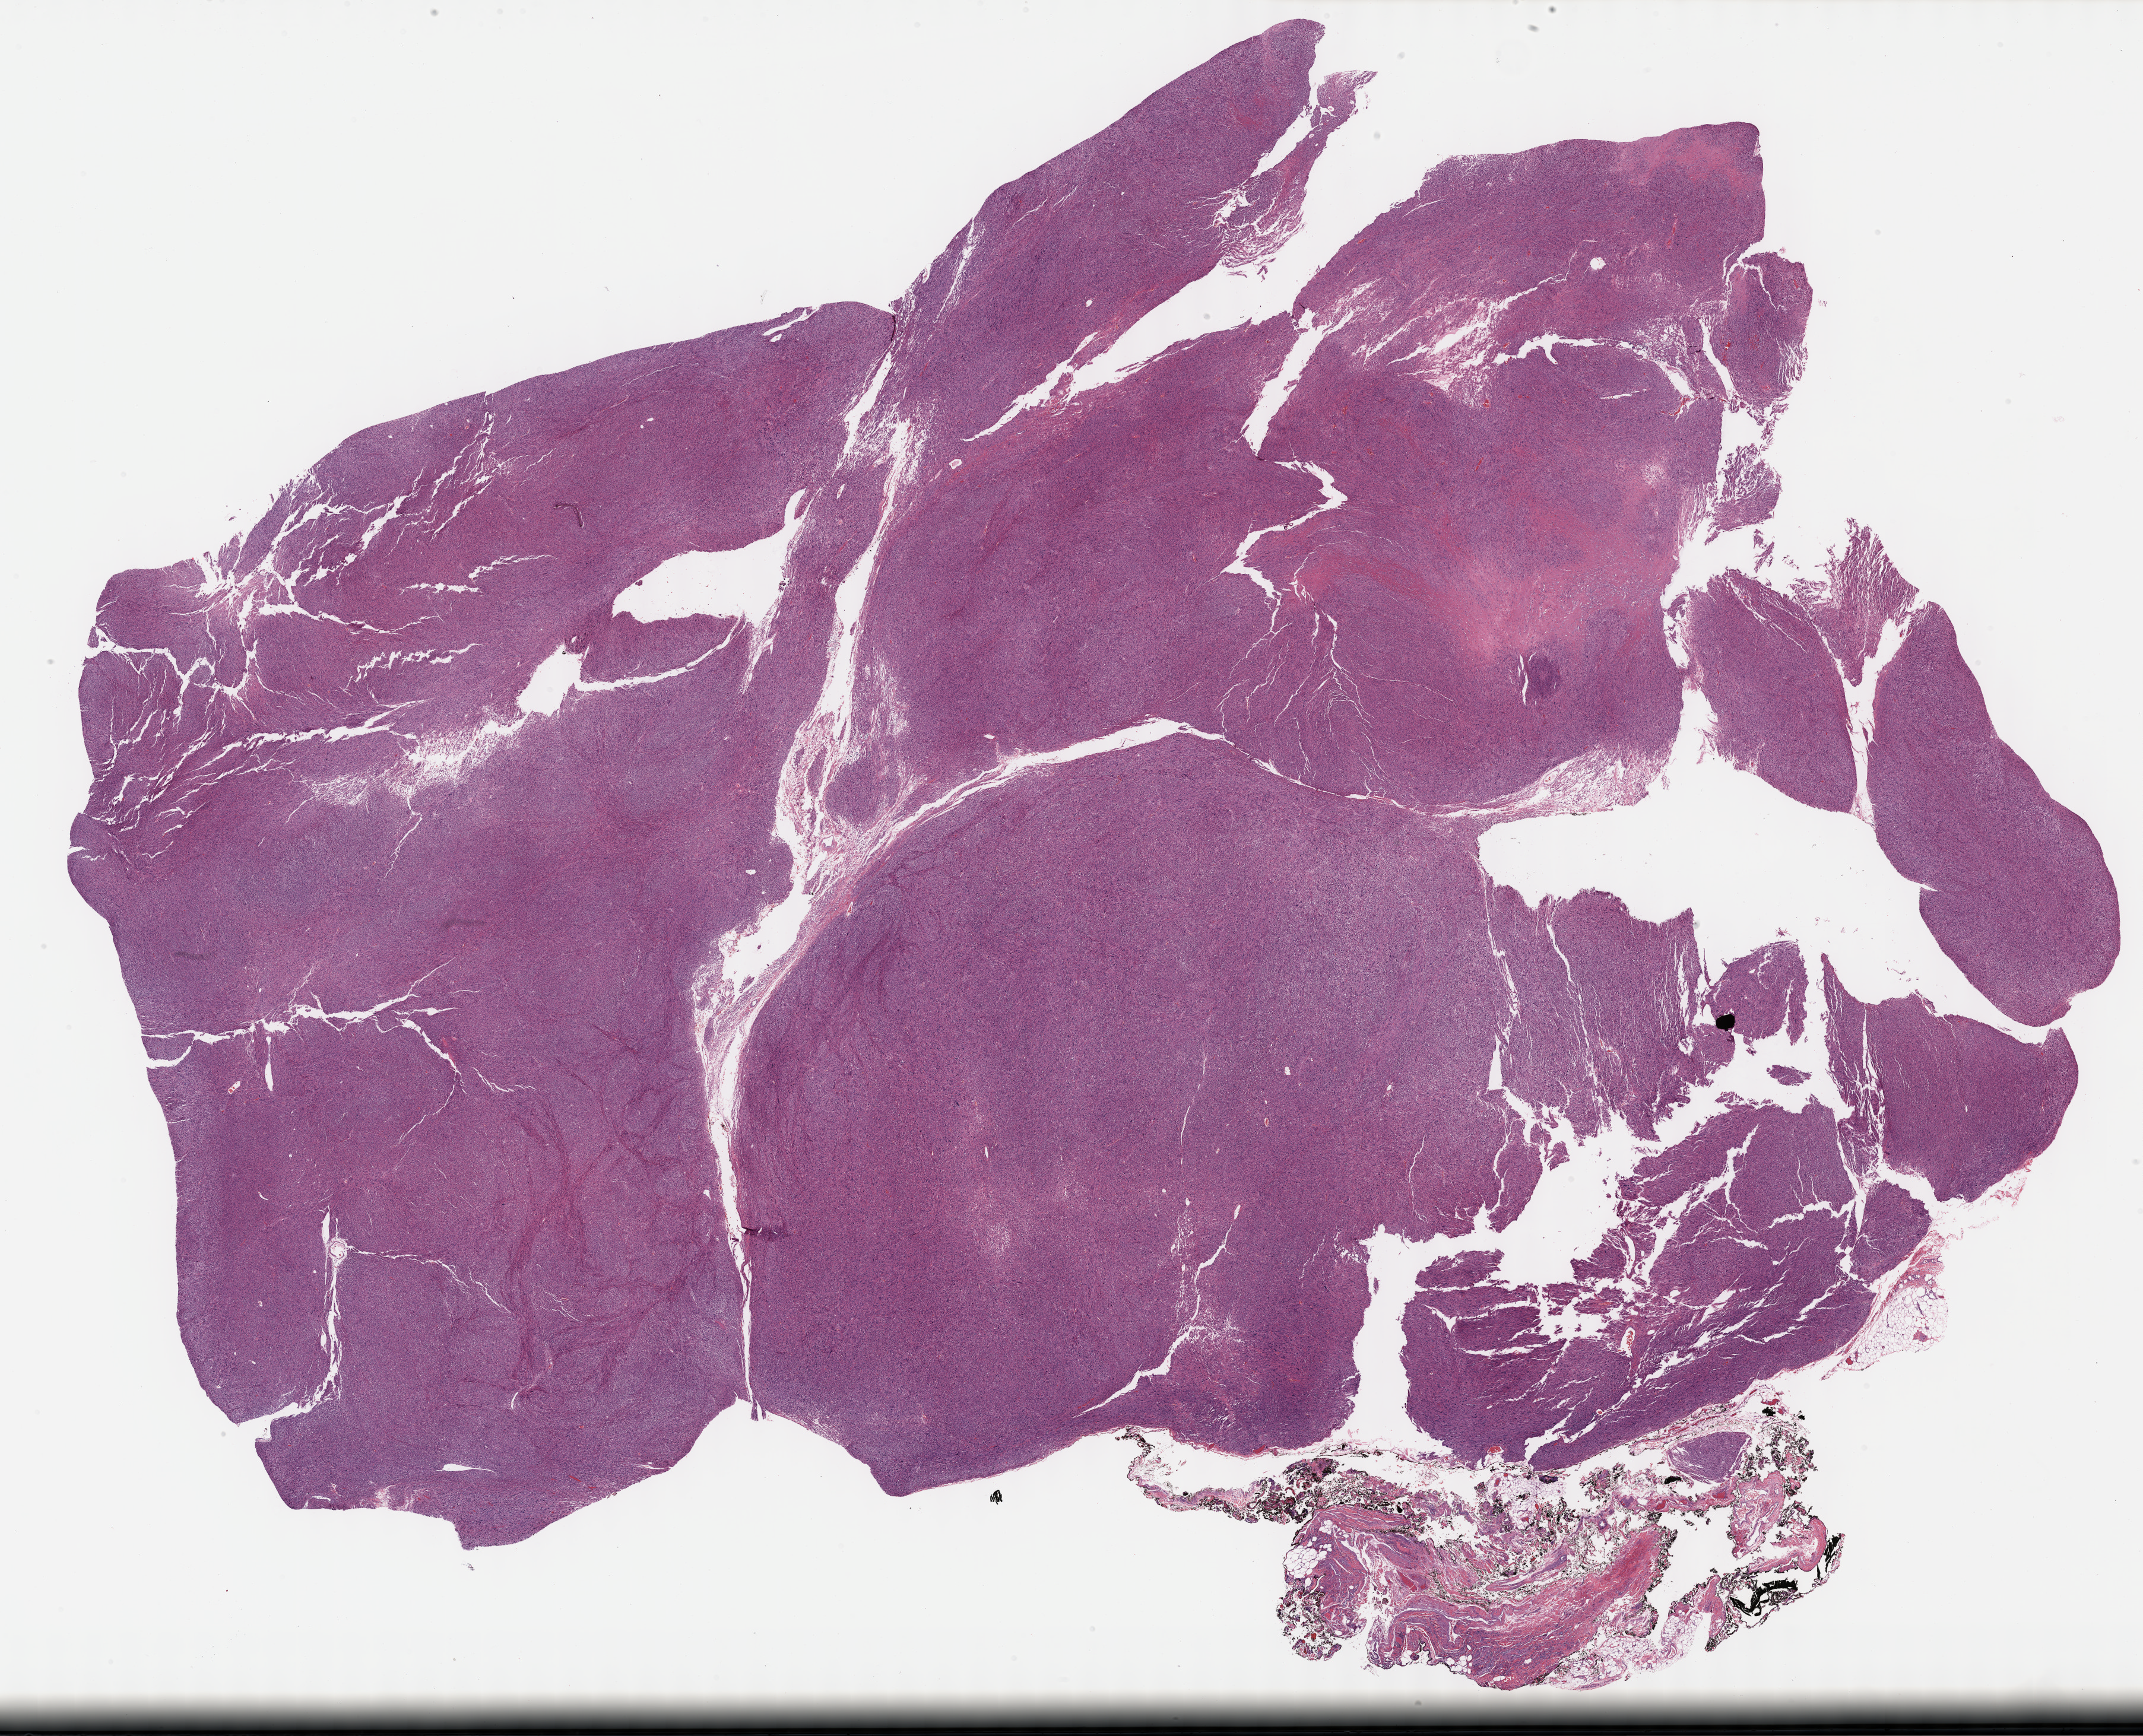
Digitized H&E tissue section (whole slide) — low-resolution overview of the scanned area, about 29.2 x 23.7 mm; formalin-fixed paraffin-embedded (FFPE) diagnostic section; retroperitoneum and peritoneum, primary tumour sample. Patient: male, age at initial diagnosis 57 years.
Histologic diagnosis: Leiomyosarcoma, NOS (retroperitoneum).